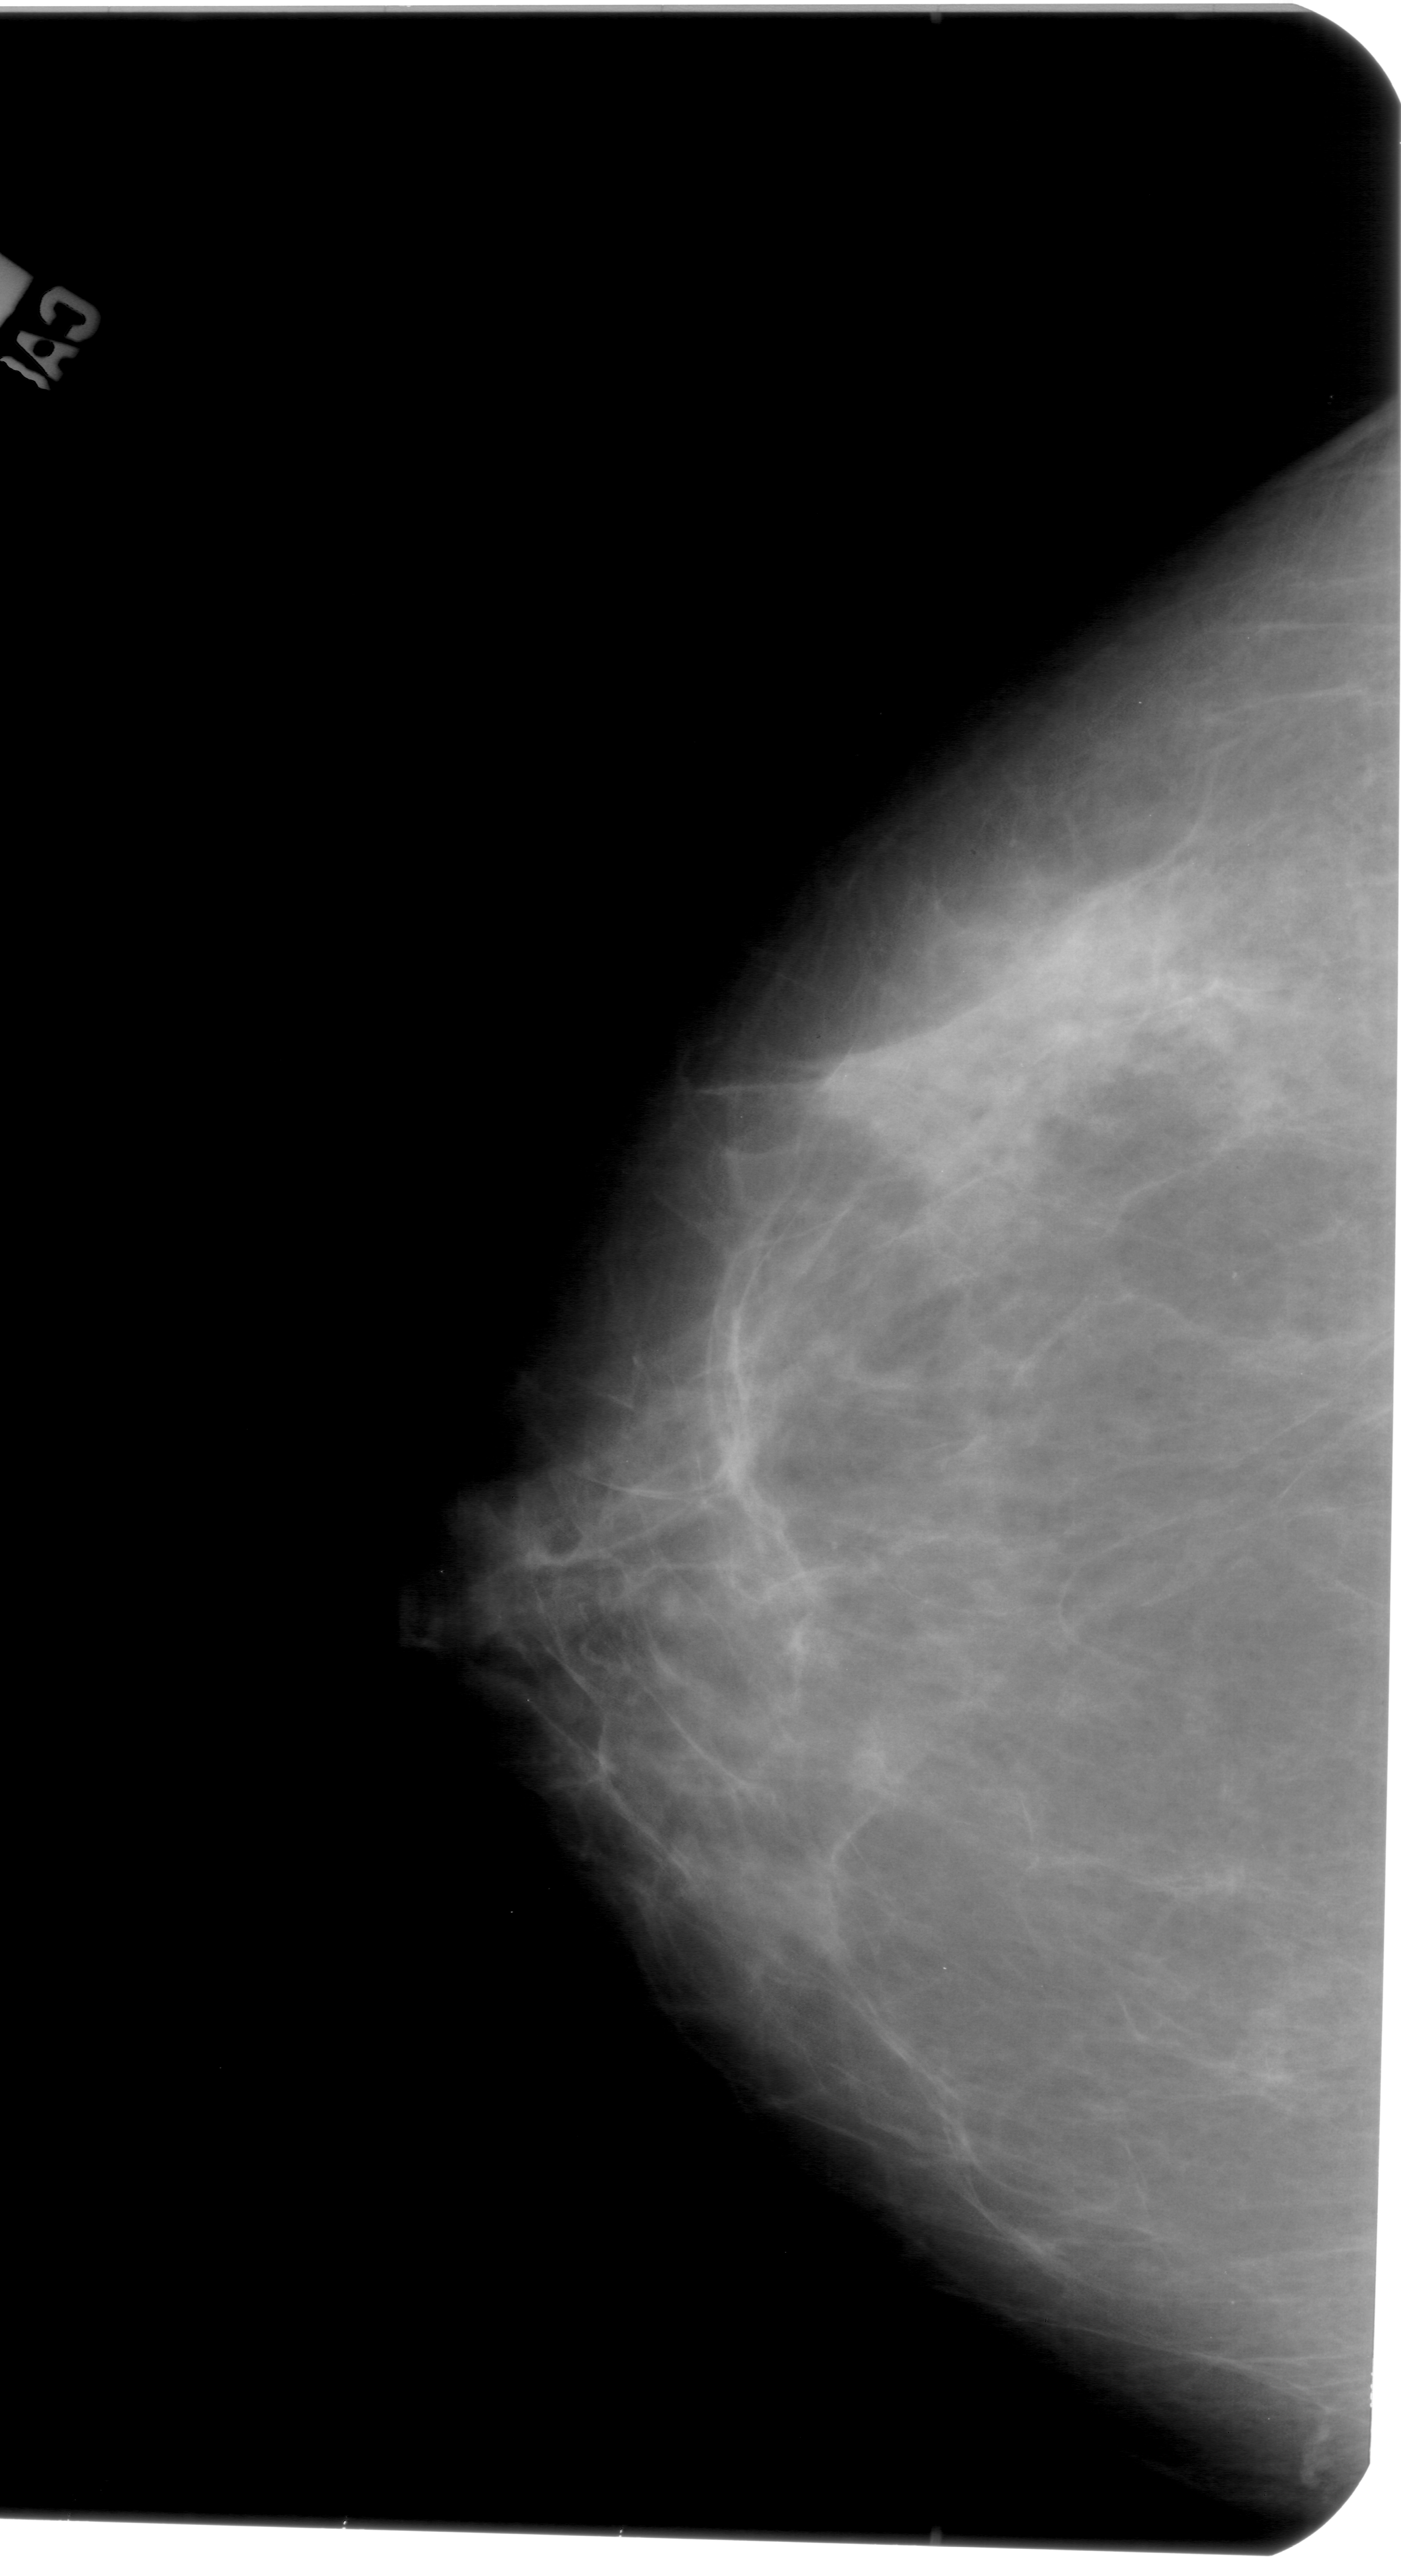
Digitized screen-film mammogram; left breast; craniocaudal (CC) view; BI-RADS breast density category 3 (scale 1–4).
Marked findings (only marked abnormalities are described; nothing is implied about the rest of the image): calcifications, morphology pleomorphic, distribution clustered; BI-RADS assessment category 4; pathology (as recorded): benign.